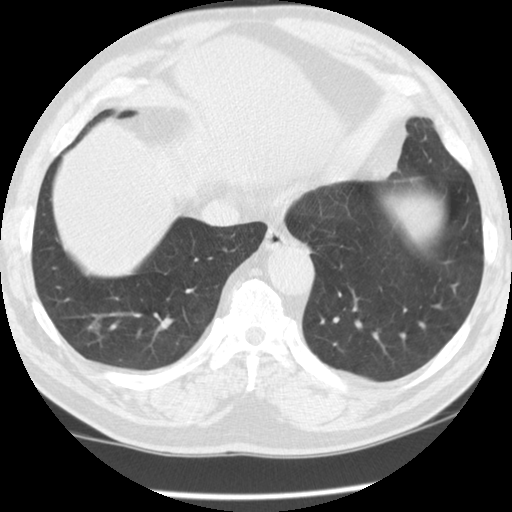
Low-dose screening chest CT, one axial slice; slice 27 of 115 in the series (ordered by position); reconstruction kernel STANDARD; 120 kVp; lung window (W 1500 / L -600 HU); 2.5 mm slice thickness; 512 × 512 image matrix, field of view 330 × 330 mm.
Structures marked on this image (expert manual segmentation):
- lesion 1 (tumor, lower lobe of right lung): box from (x=87, y=321) to (x=100, y=335) px